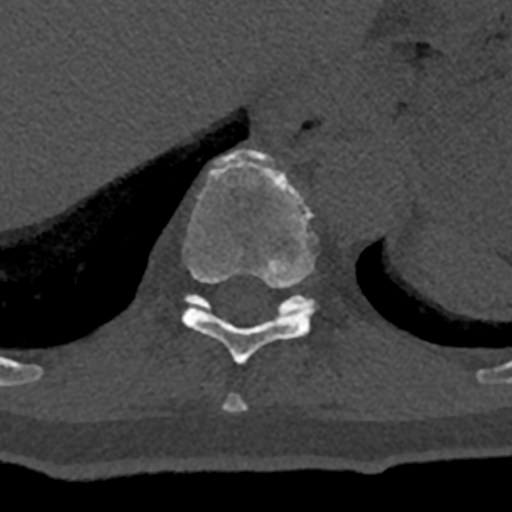
CT including the spine, one axial slice. Slice 593 of 797 in the series (ordered by position). Reconstruction kernel Br40s/3. 120 kVp. Bone window (W 1800 / L 400 HU). 0.5 mm slice thickness. 512 × 512 image matrix, field of view 160 × 160 mm. Patient: male, 74 years. Case-level facts recorded for this patient, not image findings: primary cancer: renal.
Structures marked on this image (semi-automatic segmentation, software-assisted and operator-edited):
- T10 vertebra: bounding box [x1, y1, x2, y2] px = [182, 150, 319, 365]
- T11 vertebra: [184, 293, 316, 319]
- T9 vertebra: [224, 394, 247, 412]